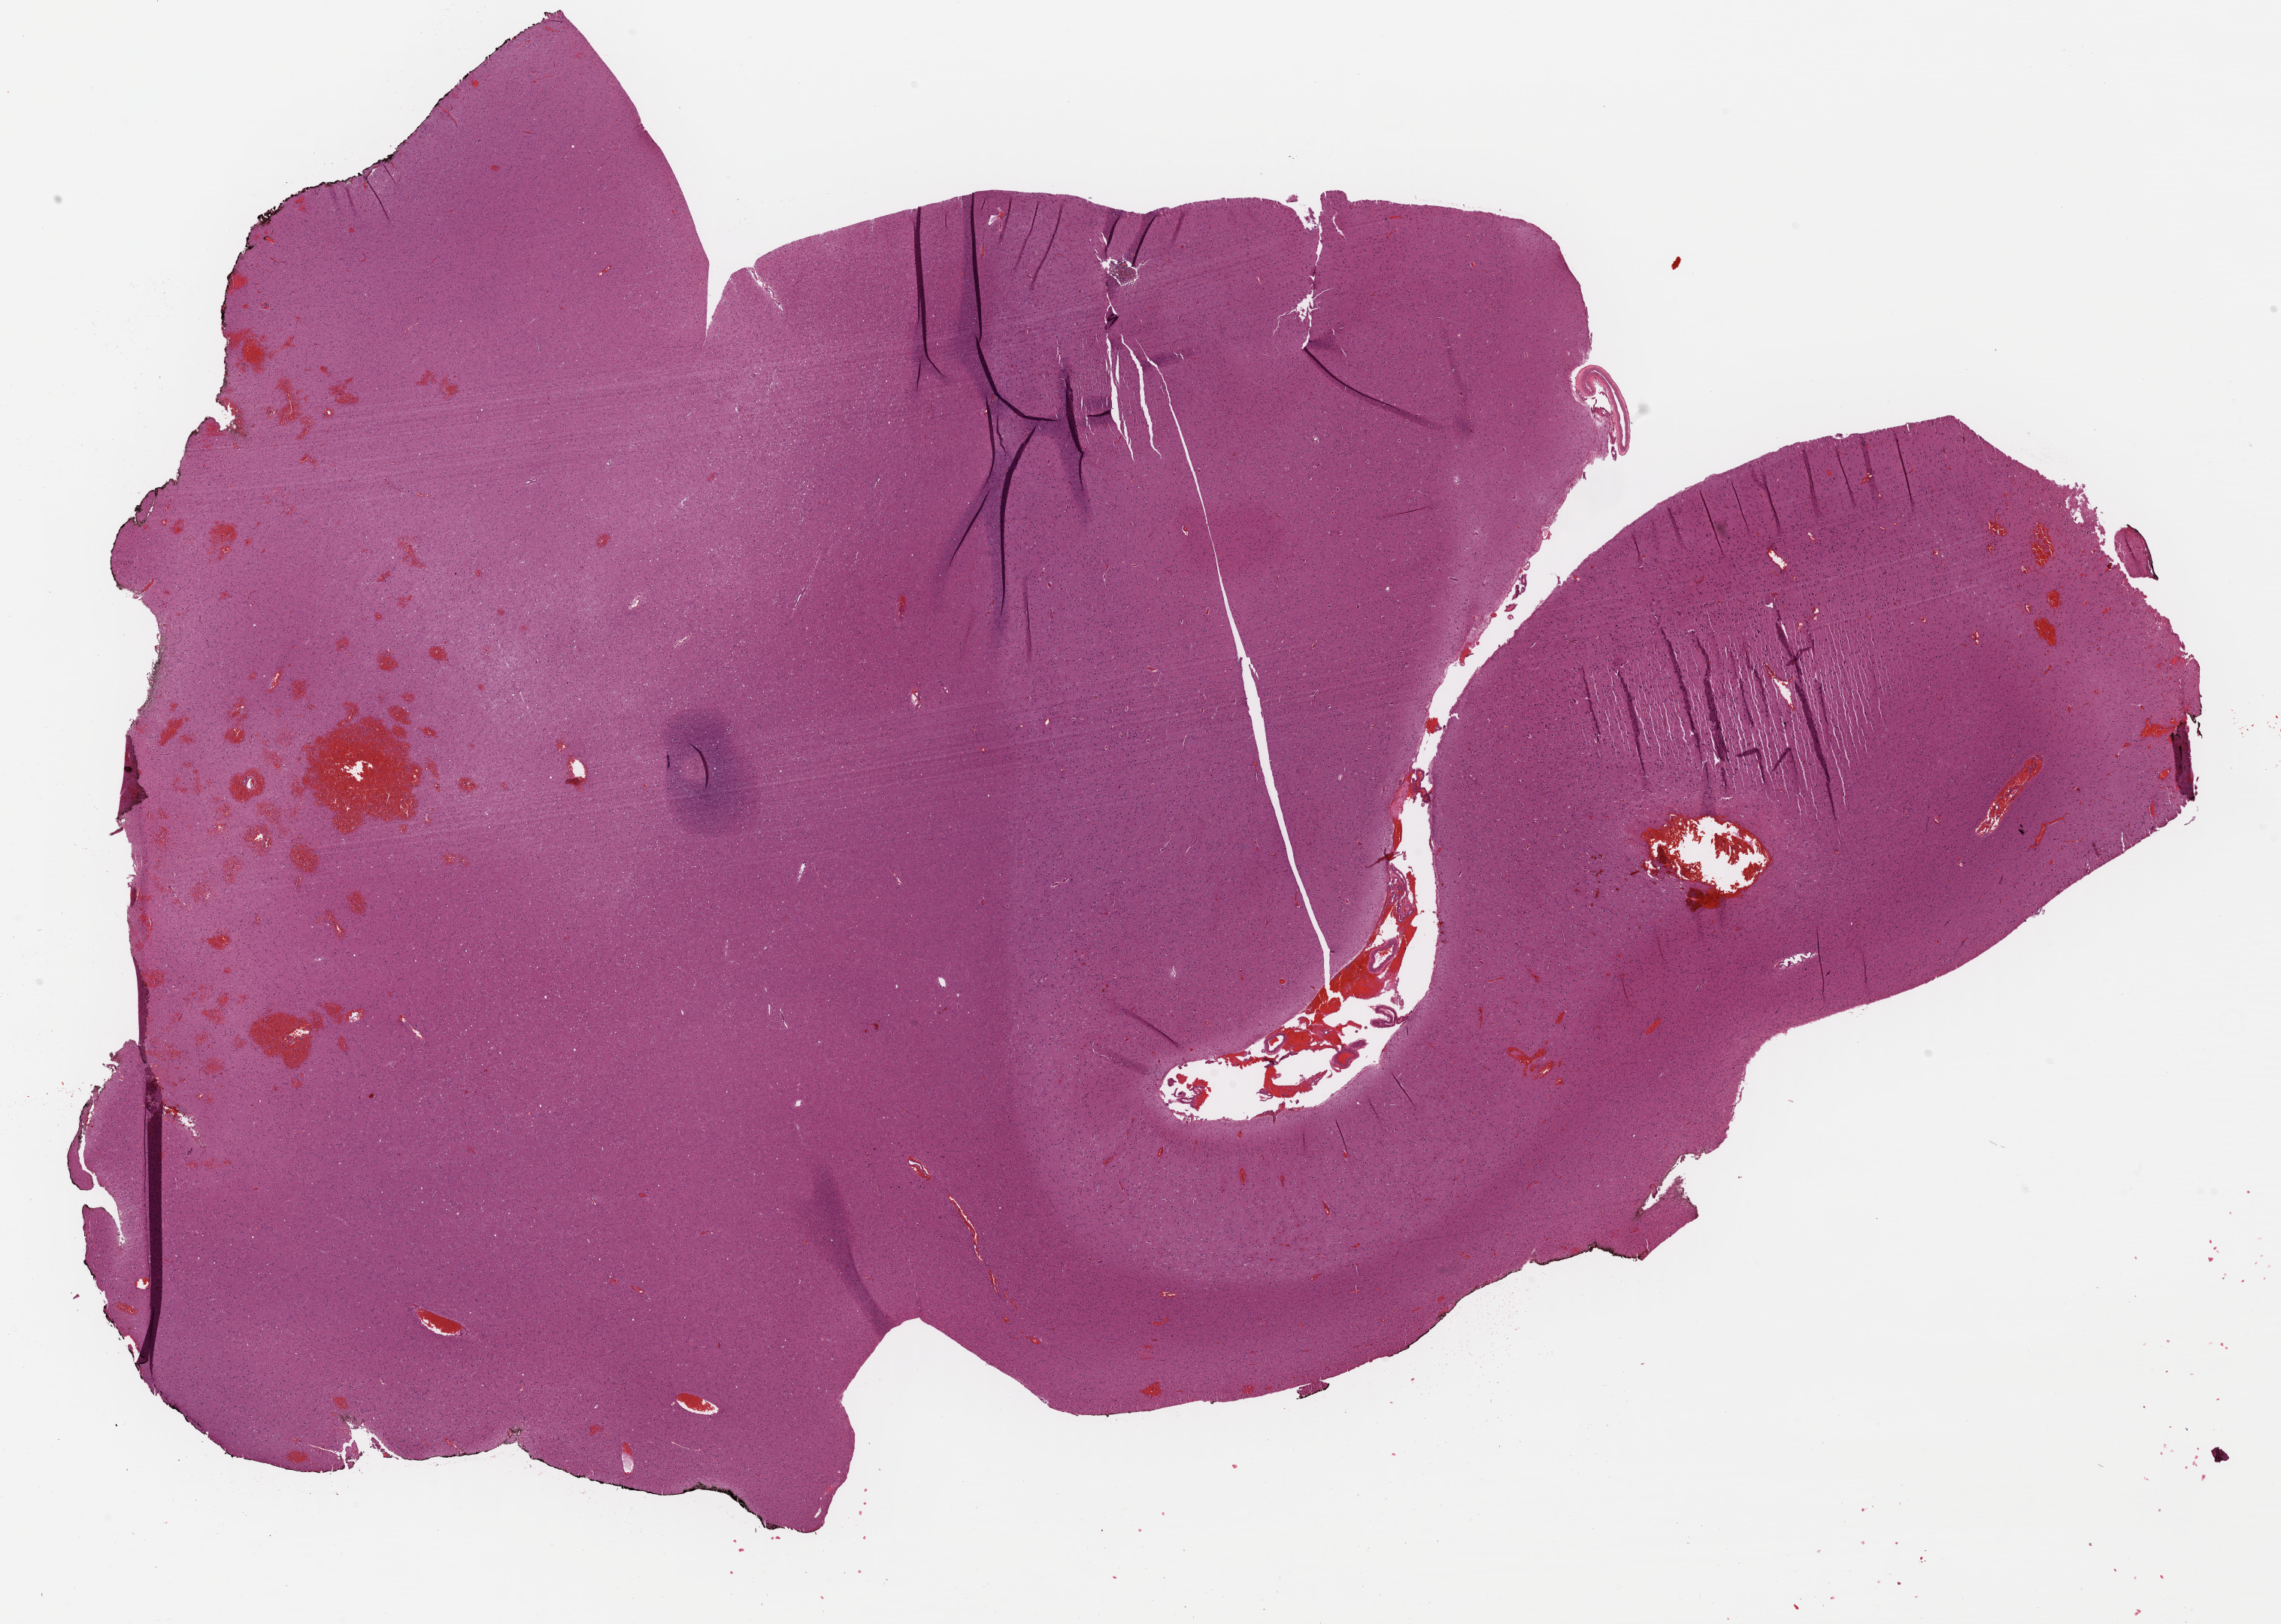
Whole-slide histology image, H&E, shown as a low-resolution overview of the whole scanned area (about 23.8 x 17.0 mm, acquisition: 40x scan); FFPE section; sample: primary tumour, brain. Patient: female, age at initial diagnosis 61 years. Histologic grade: G2 (moderately differentiated).
Diagnosis: Astrocytoma, NOS.